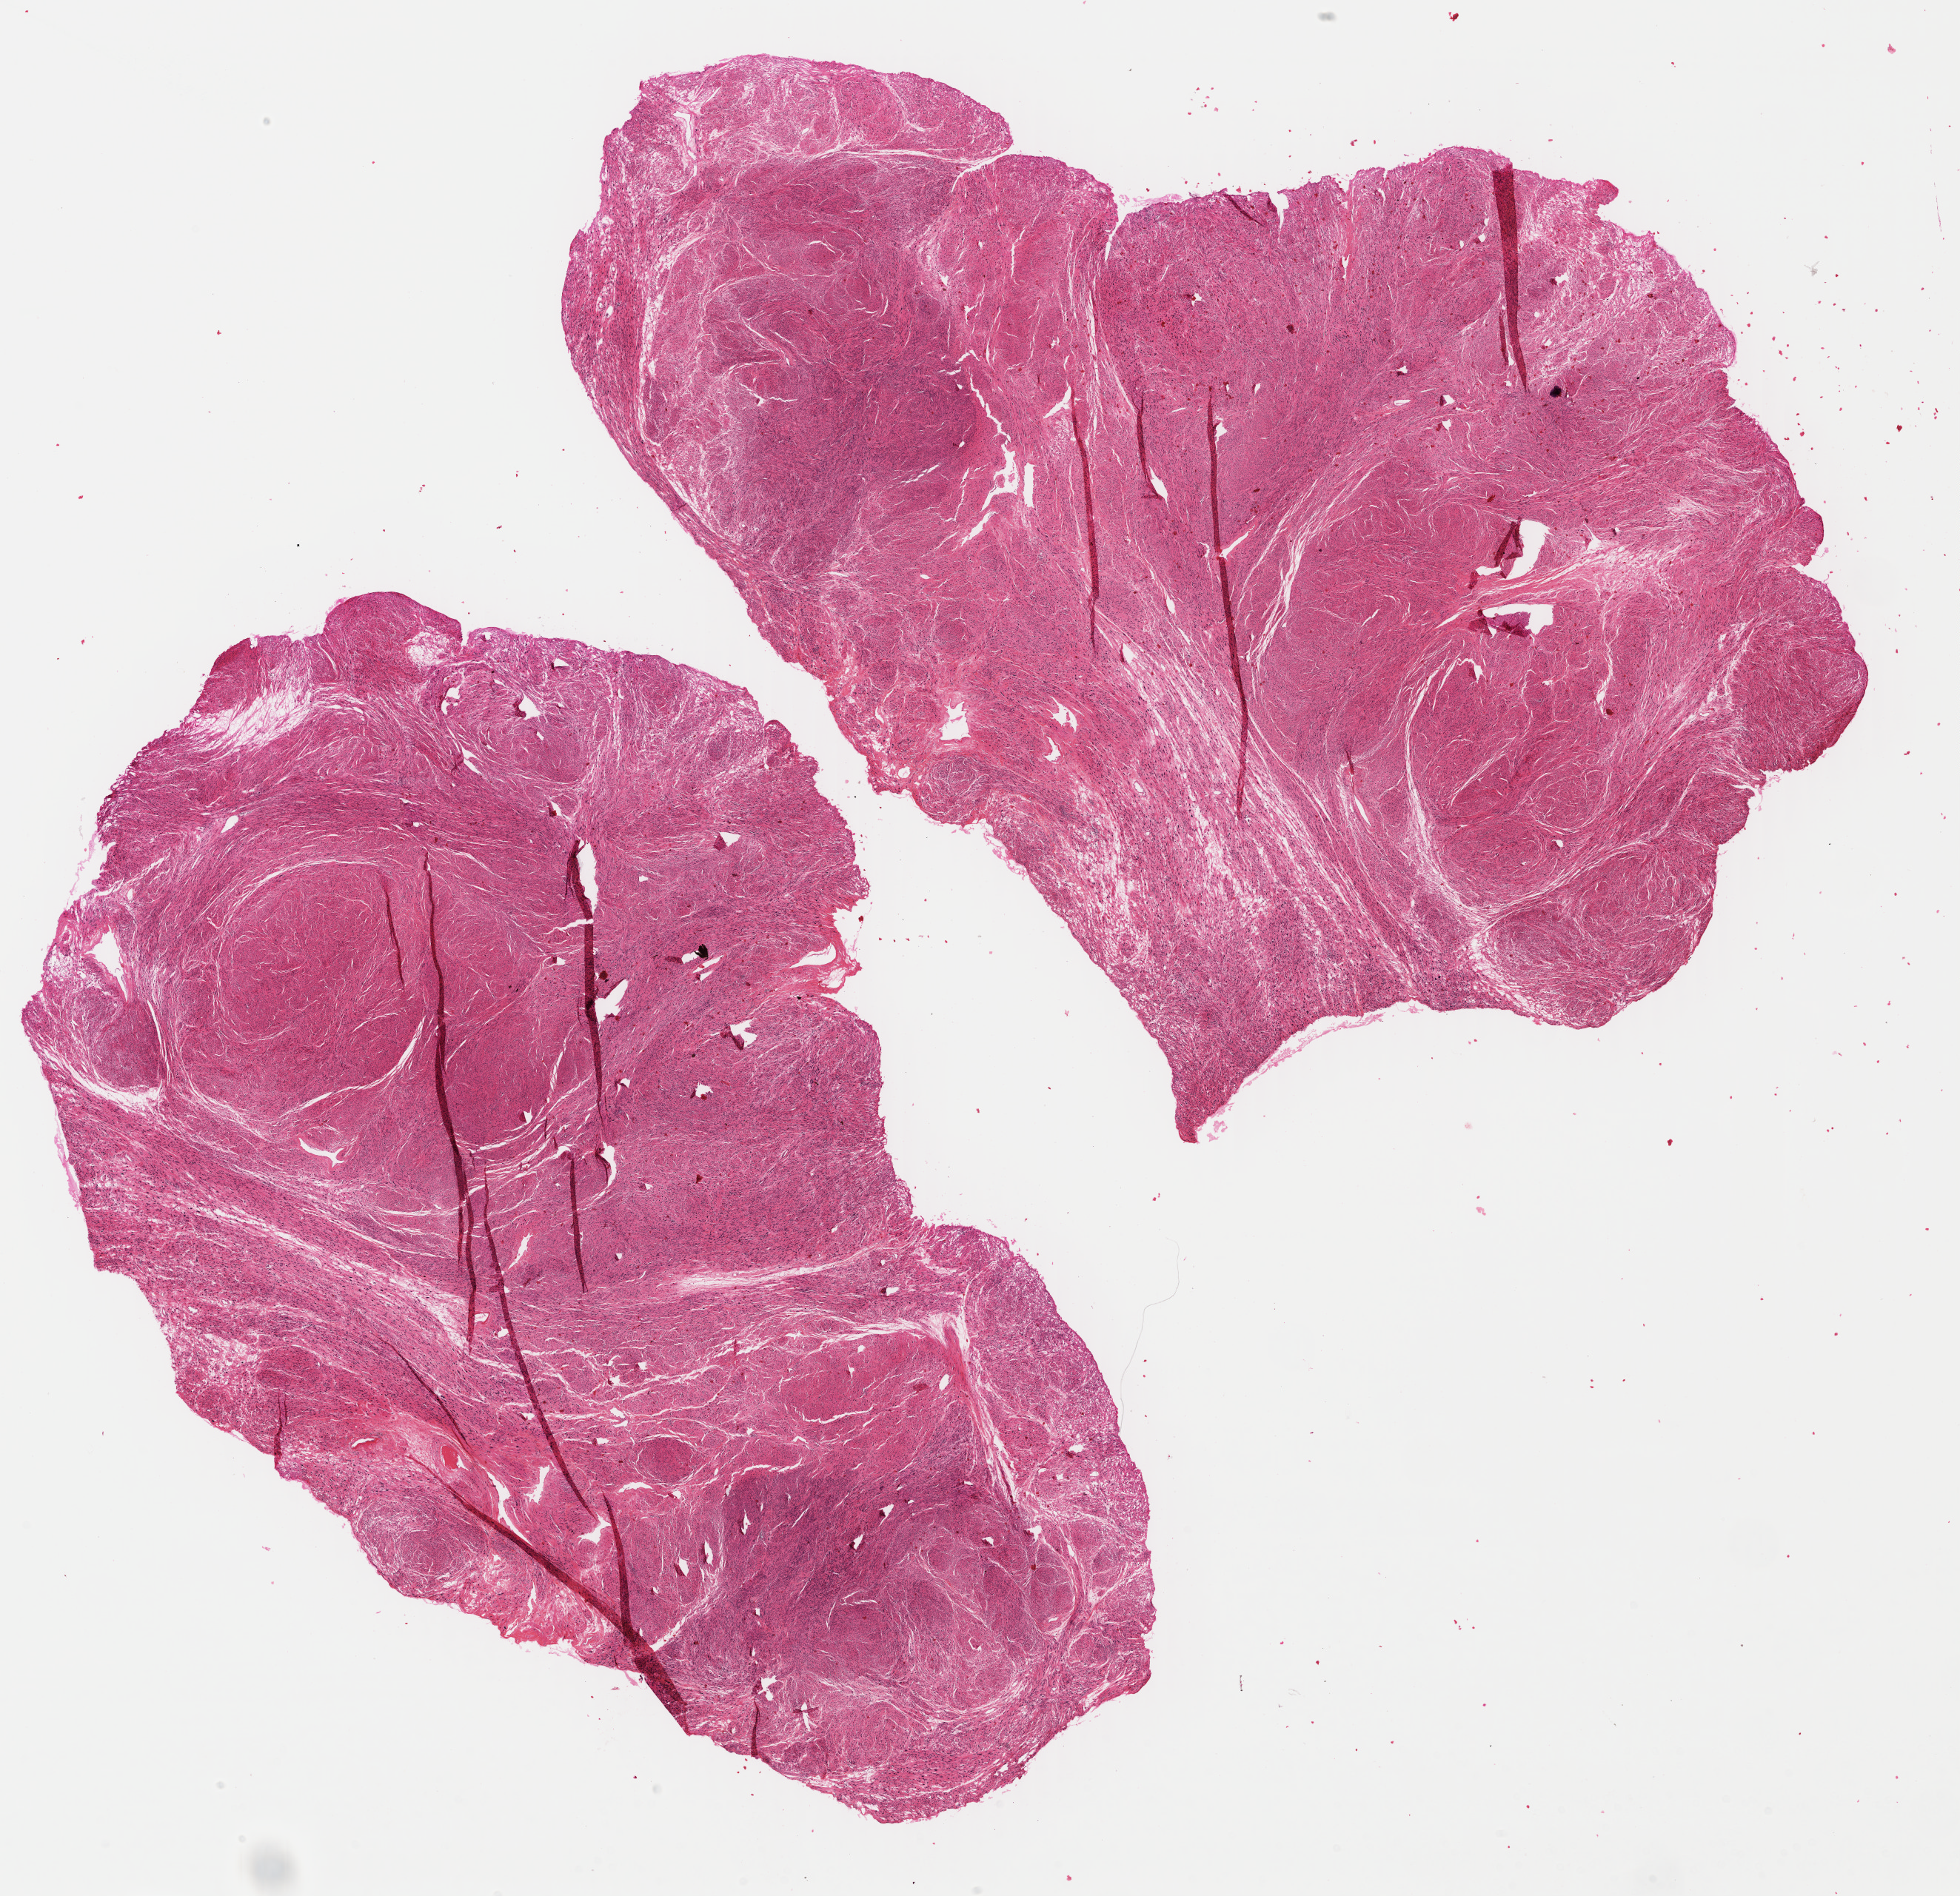
Whole-slide histology image, Hematoxylin and eosin (H&E) stained, shown as a low-resolution overview of the whole scanned area (about 20.8 x 20.1 mm, from a 40x scan); FFPE section; retroperitoneum and peritoneum, primary tumour sample. Male, age 63 years at initial diagnosis.
Diagnosis: Leiomyosarcoma, NOS (retroperitoneum).